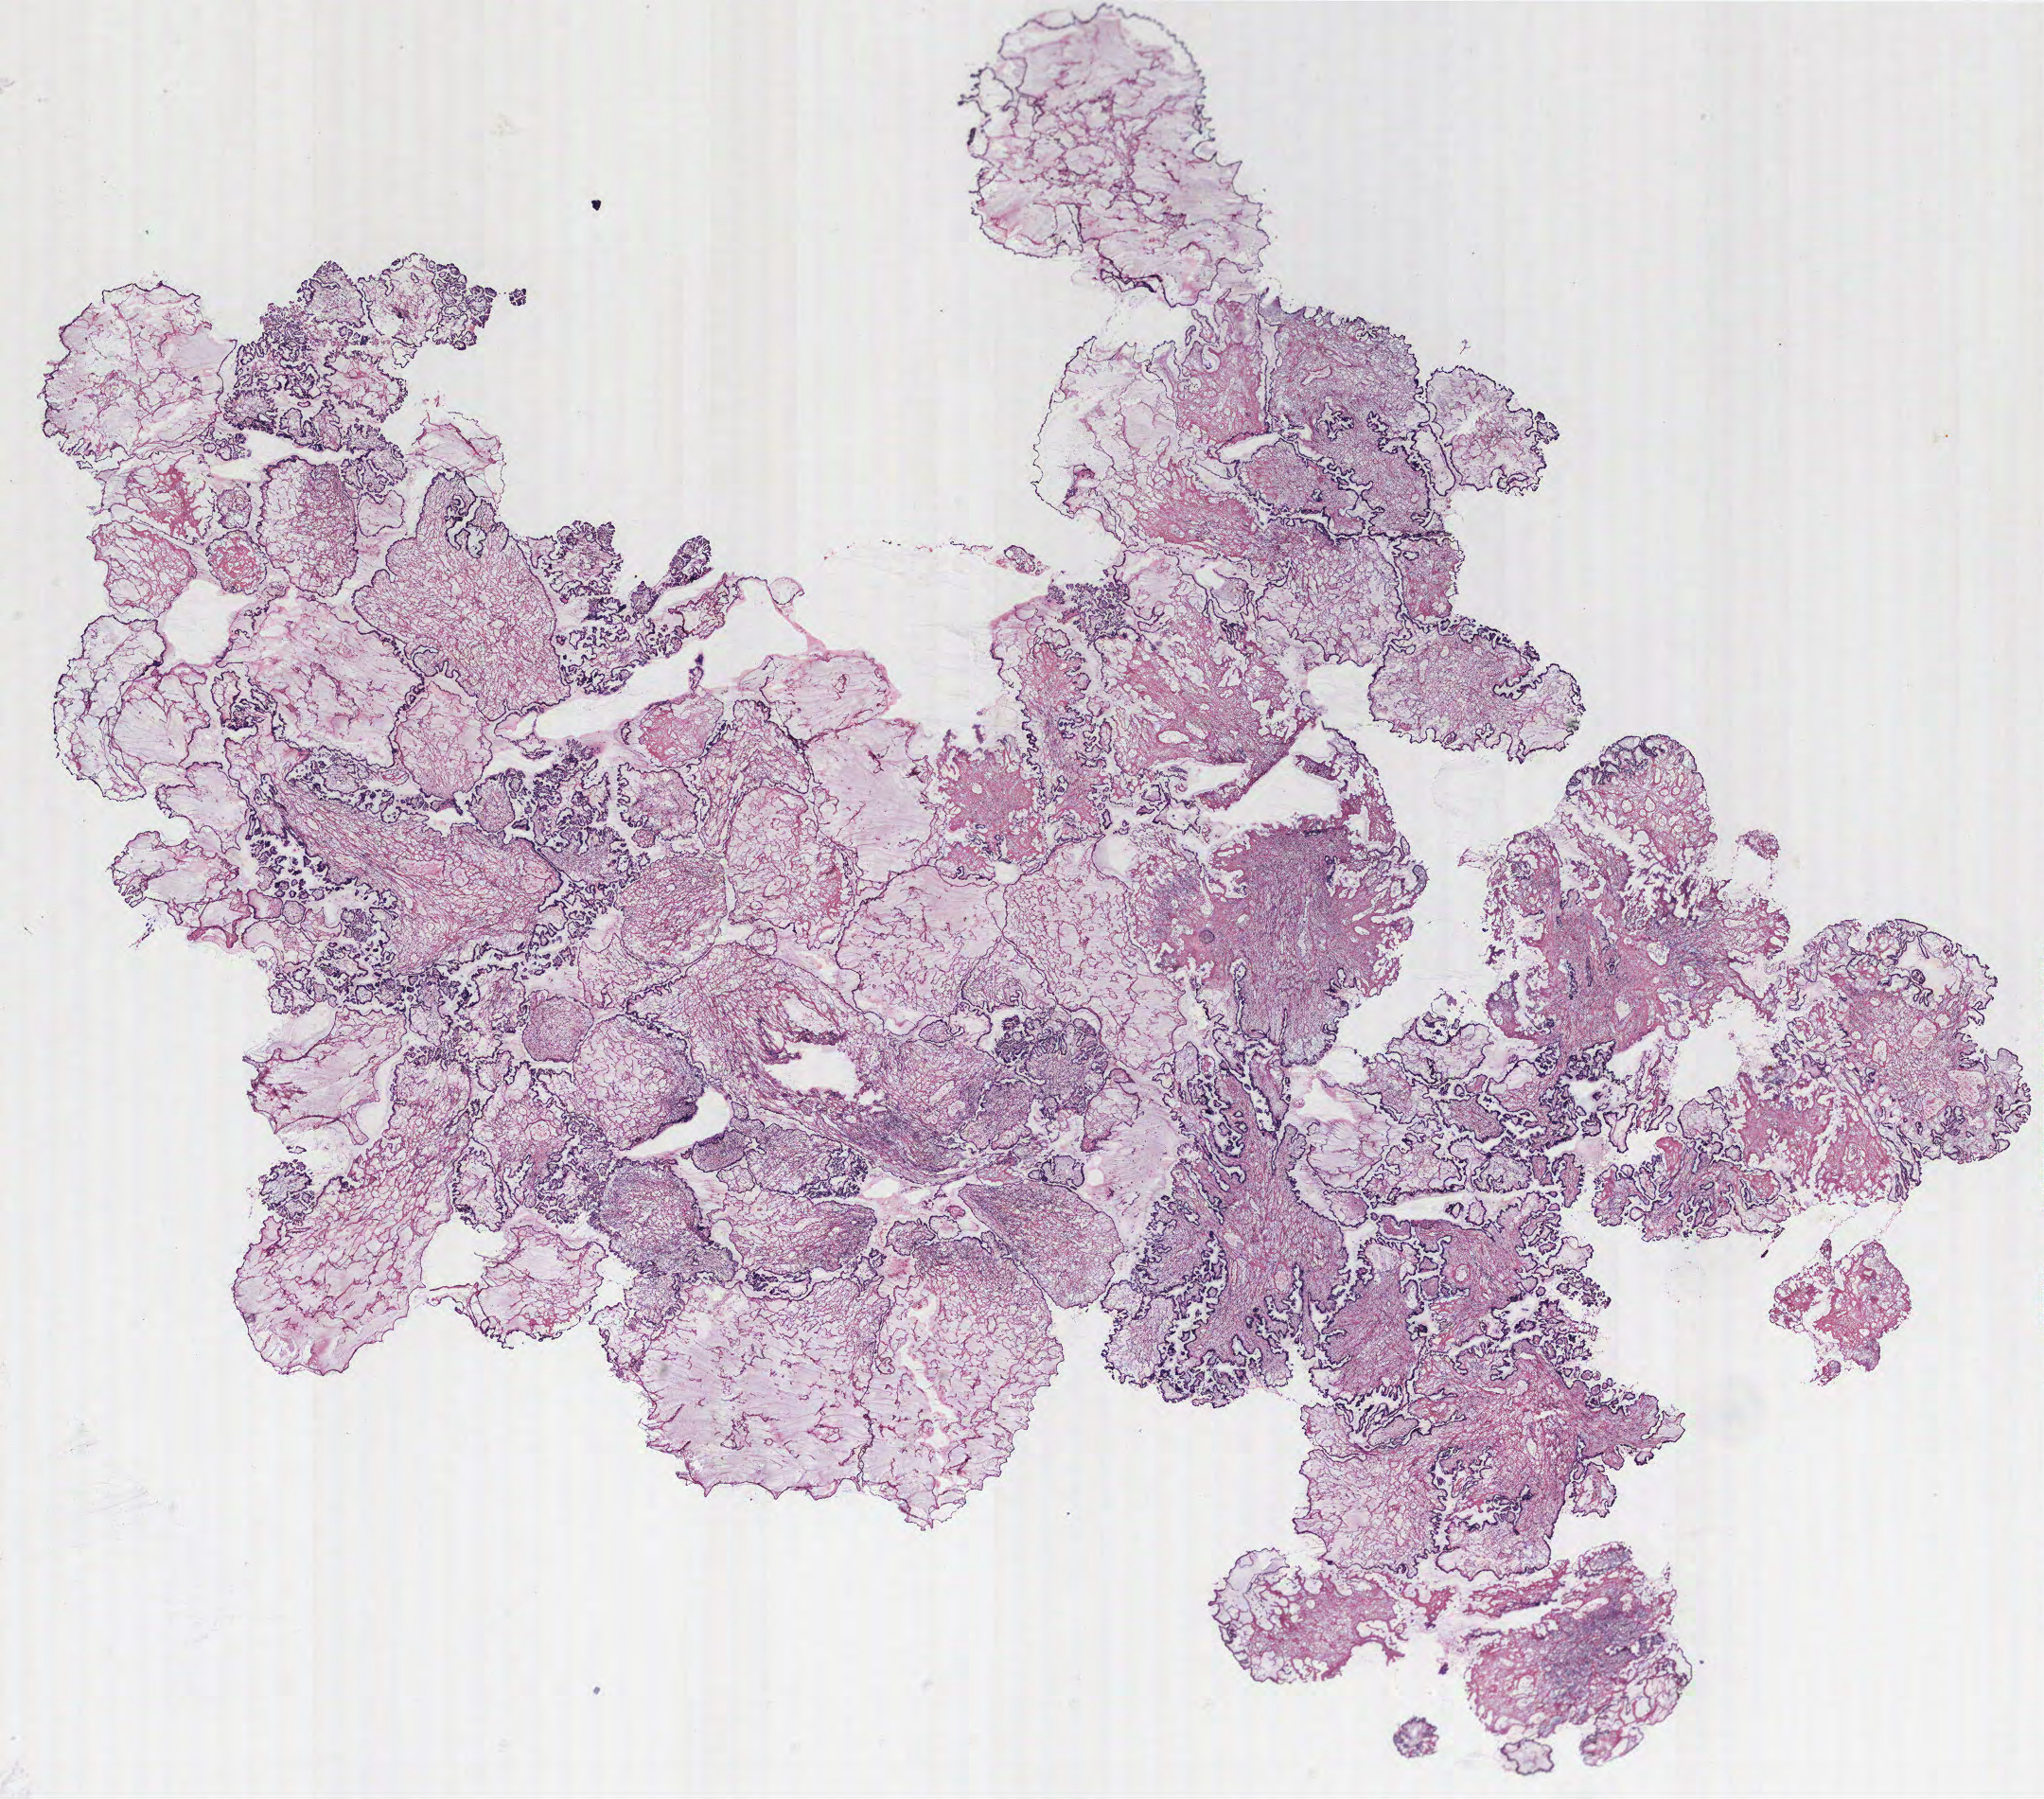
Digitized H&E tissue section (whole slide), a low-resolution overview of the entire scanned area, about 17.3 x 15.2 mm; tumour tissue sample, ovary. Patient: female, age 49 years.
• primary tumour site (as recorded): ovary
• diagnosis: Serous adenocarcinoma, NOS